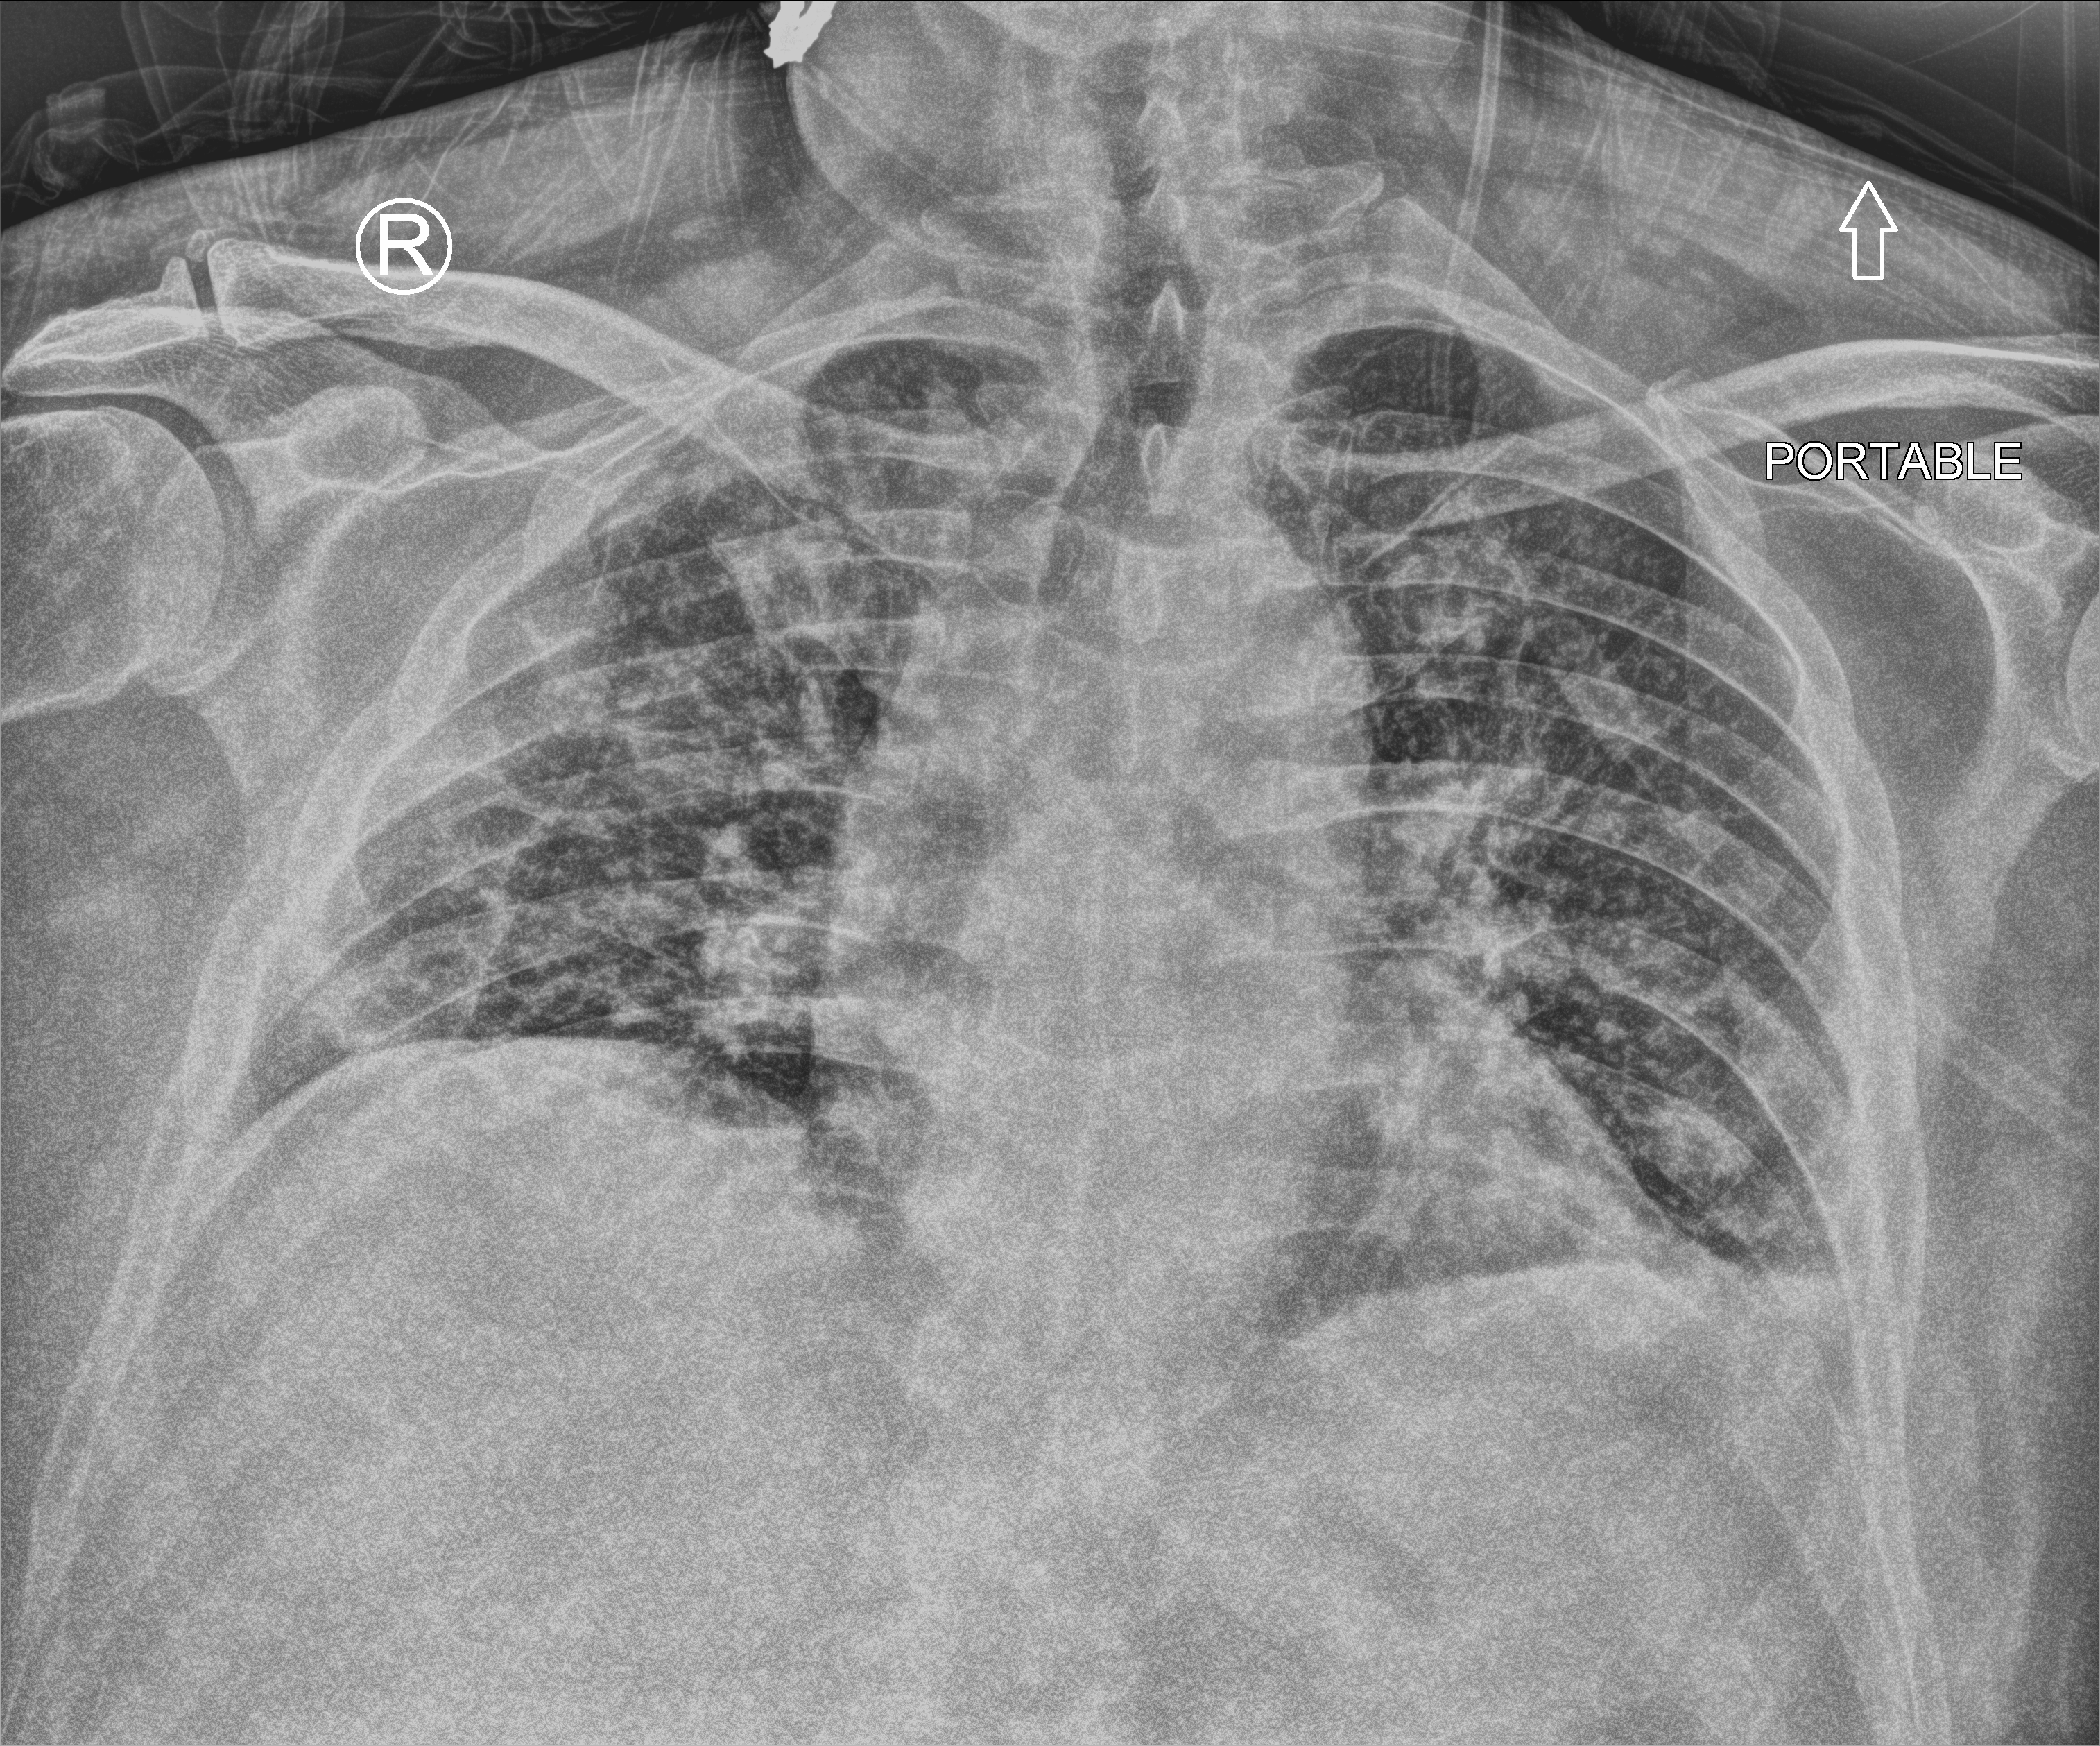
Chest X-ray (portable), anteroposterior (AP) projection. Male patient hospitalised with COVID-19, age 18–59 years.
From the hospital-stay record, not from the radiograph (when in the stay this image was taken is not recorded): mechanically ventilated during this hospital stay: no; length of hospital stay: 8 days; COPD (admission record): no.